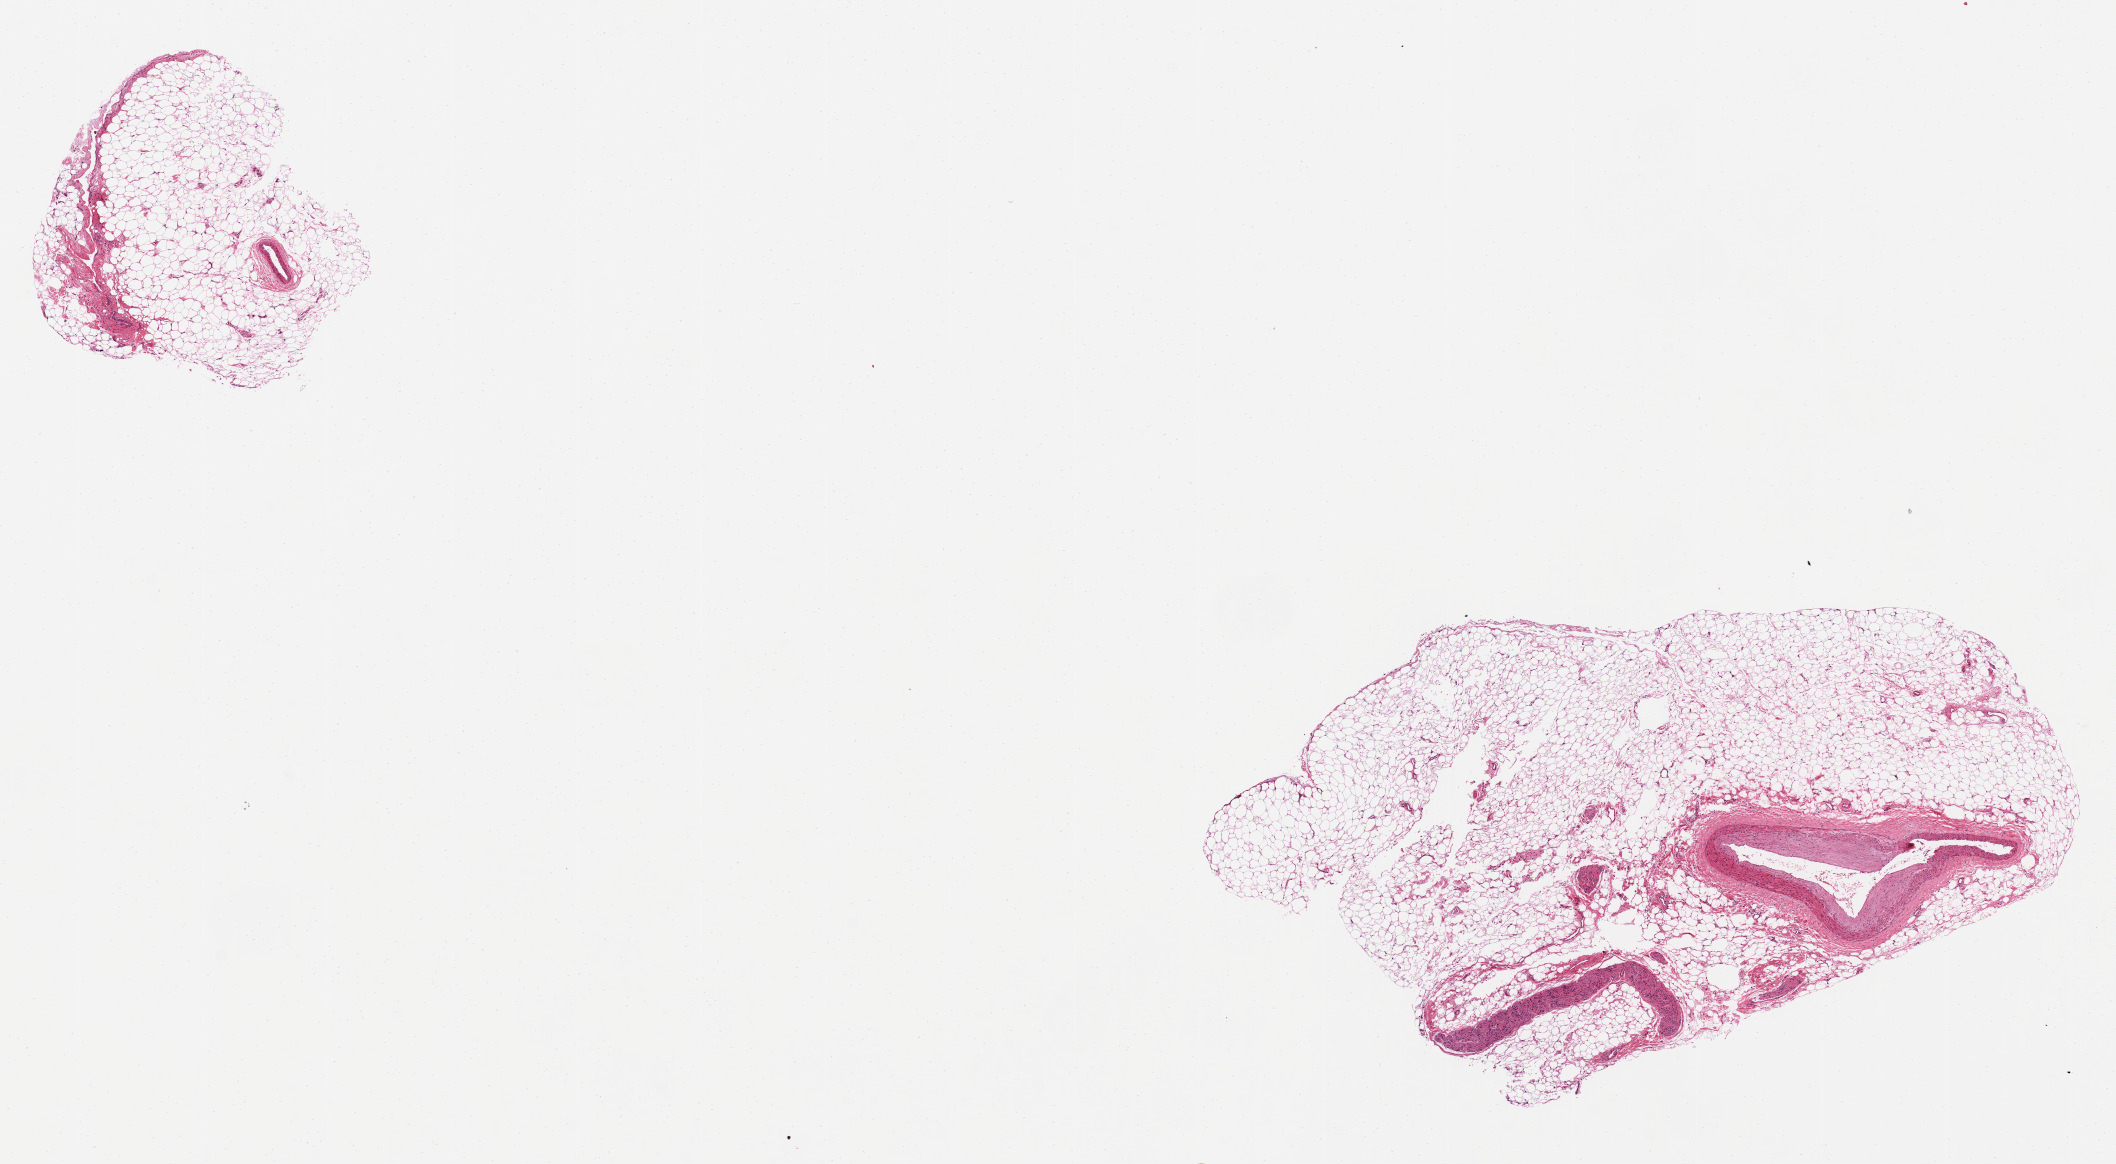
Whole-slide image, haematoxylin and eosin stain, brightfield, whole scanned area (about 16.7 x 9.2 mm) shown as a low-resolution overview. PAXgene-fixed paraffin-embedded (PFPE) section. Sampled site (target tissue): coronary artery. Tissue donor sample. Donor sex: male.
Review note (as recorded): Small artery, 2.6 x 1mm, with large eccentric plaque in 6.8x3.8mm adipose tissue containing small nerve. Artery is 10% of aliquot. Also separate 2.7x2.6mm fat tissue with very small 0.4x0.2 vessel.